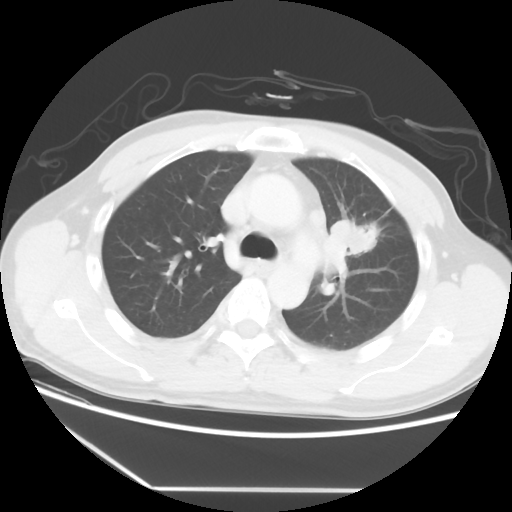
Chest CT, one axial slice; position 38 of 56 along the scan axis; reconstruction kernel STANDARD; 120 kVp; lung window (W 1500 / L -600 HU); 5 mm slice thickness; 512 × 512 image matrix. Patient: male, 53 years. Case-level facts recorded for this patient, not image findings: clinical TNM (as recorded): T2a N1 M1b.
Outlined on this slice (bounding box drawn by a radiologist):
- lung tumour (recorded histology: adenocarcinoma): bounding box <330,213,376,259> (left, top, right, bottom; pixels)